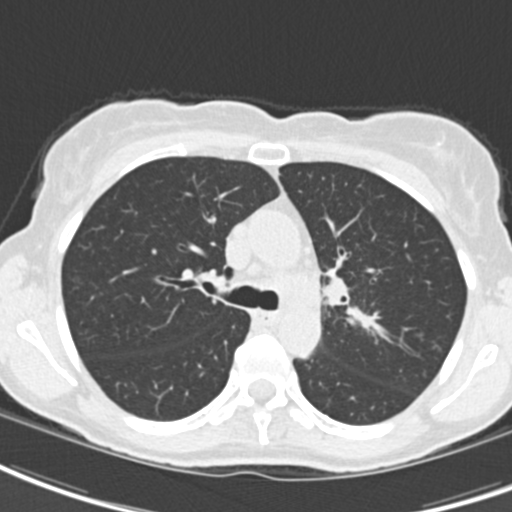
Axial slice from a low-dose chest CT screening exam, baseline screening round, lung window (W 1500 / L -600 HU), standard (soft-tissue) reconstruction kernel (B30f). Female participant, aged 62 years at enrolment. Current smoker at enrolment.
Expert-annotated lung lesion, box from (x=292, y=253) to (x=365, y=337) px. Screening reader's record for this exam (one nodule recorded; not confirmed to be the boxed lesion): non-calcified nodule or mass ≥4 mm, right upper lobe, 24 × 20 mm, smooth margins, ground glass attenuation. Note: the box lies in the patient's left hemithorax on this image, whereas the reader's record names the right lung; they may be different findings. Official screen result: positive, change unspecified: nodule(s) >= 4 mm or enlarging nodule(s), mass(es), or other non-specific abnormalities suspicious for lung cancer.